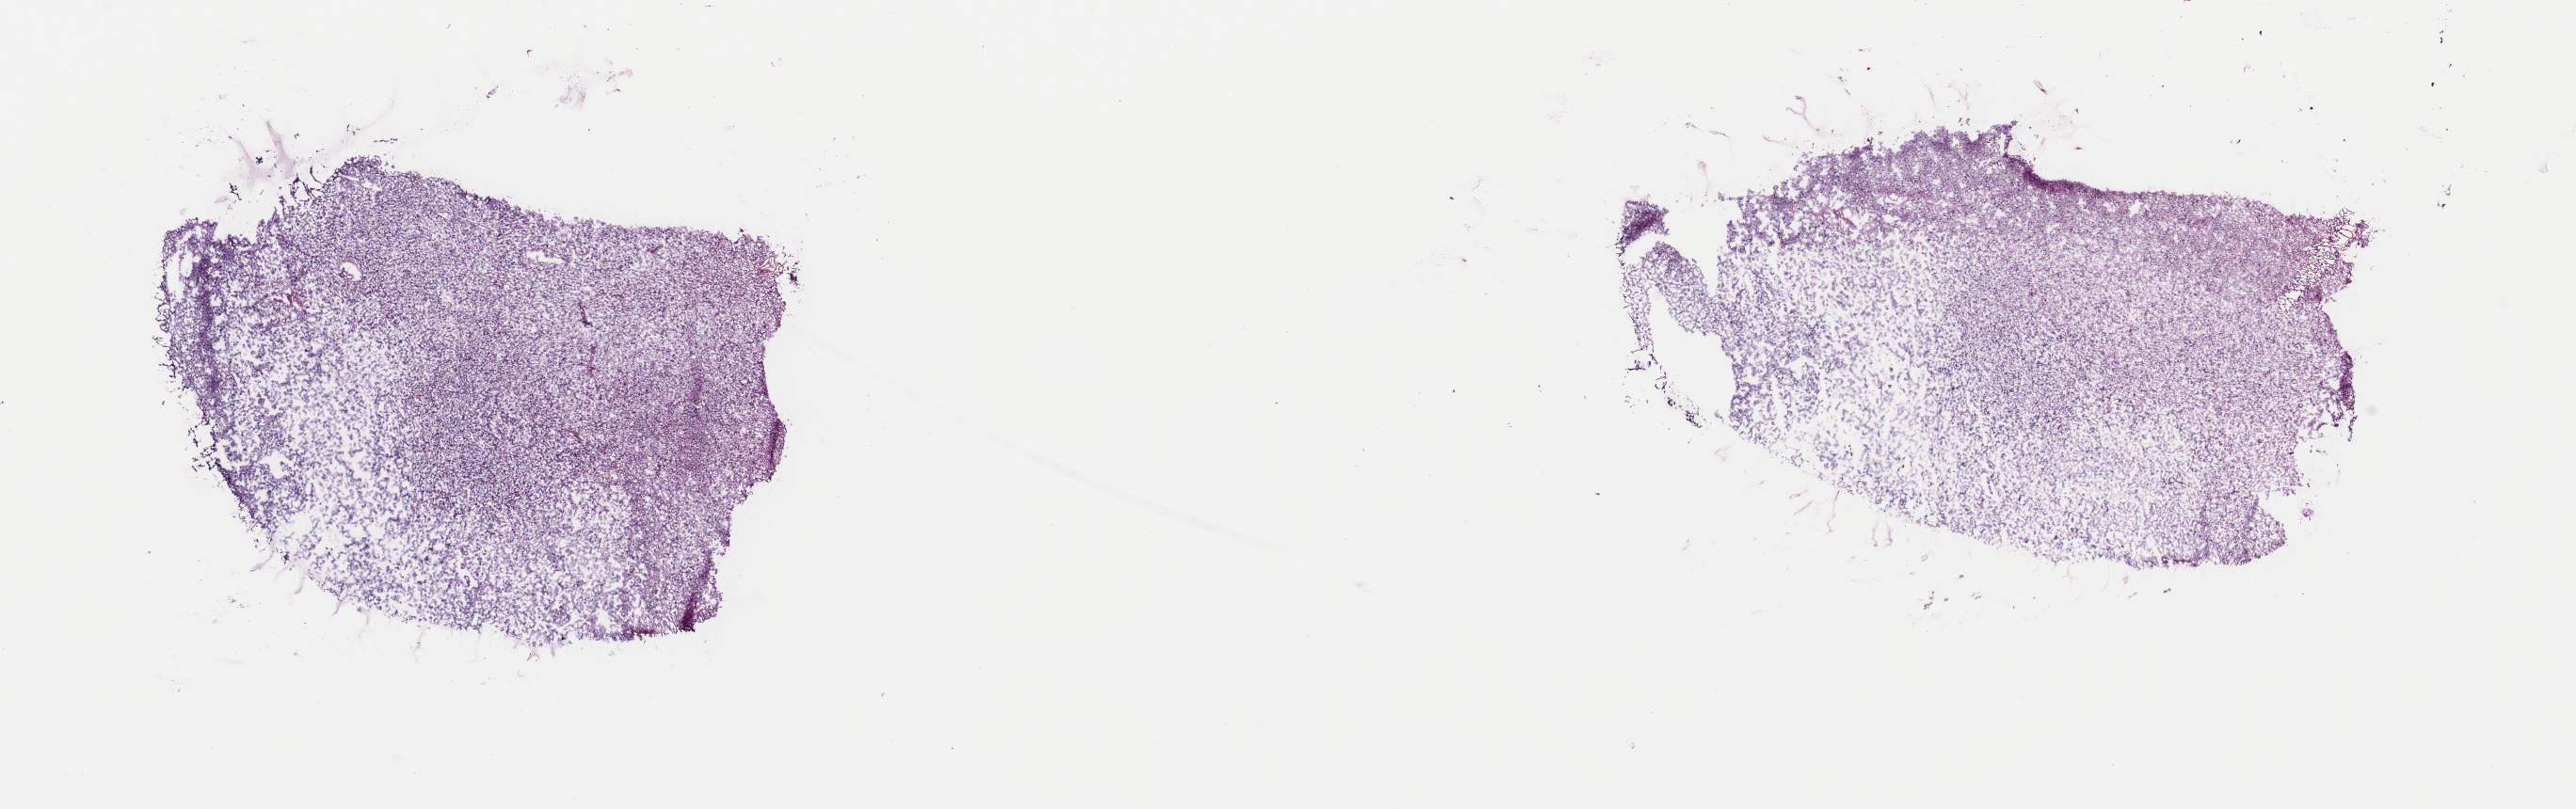
H&E-stained whole-slide image, shown as a low-resolution overview of the whole scanned area (about 21.6 x 6.8 mm, slide scanned at 40x), frozen section from the top of the tissue portion, brain, primary tumour sample. Male, age 27 years at initial diagnosis. Histologic grade: G2 (moderately differentiated). Slide review estimates, as recorded: tumour cells 50%, tumour nuclei 80%, normal cells 10%, stromal cells 40%, necrosis 0%. Infiltration values recorded for this section: lymphocyte infiltration 0%, monocyte infiltration 0%, neutrophil infiltration 0%.
• pathologic diagnosis: Mixed glioma (cerebrum)